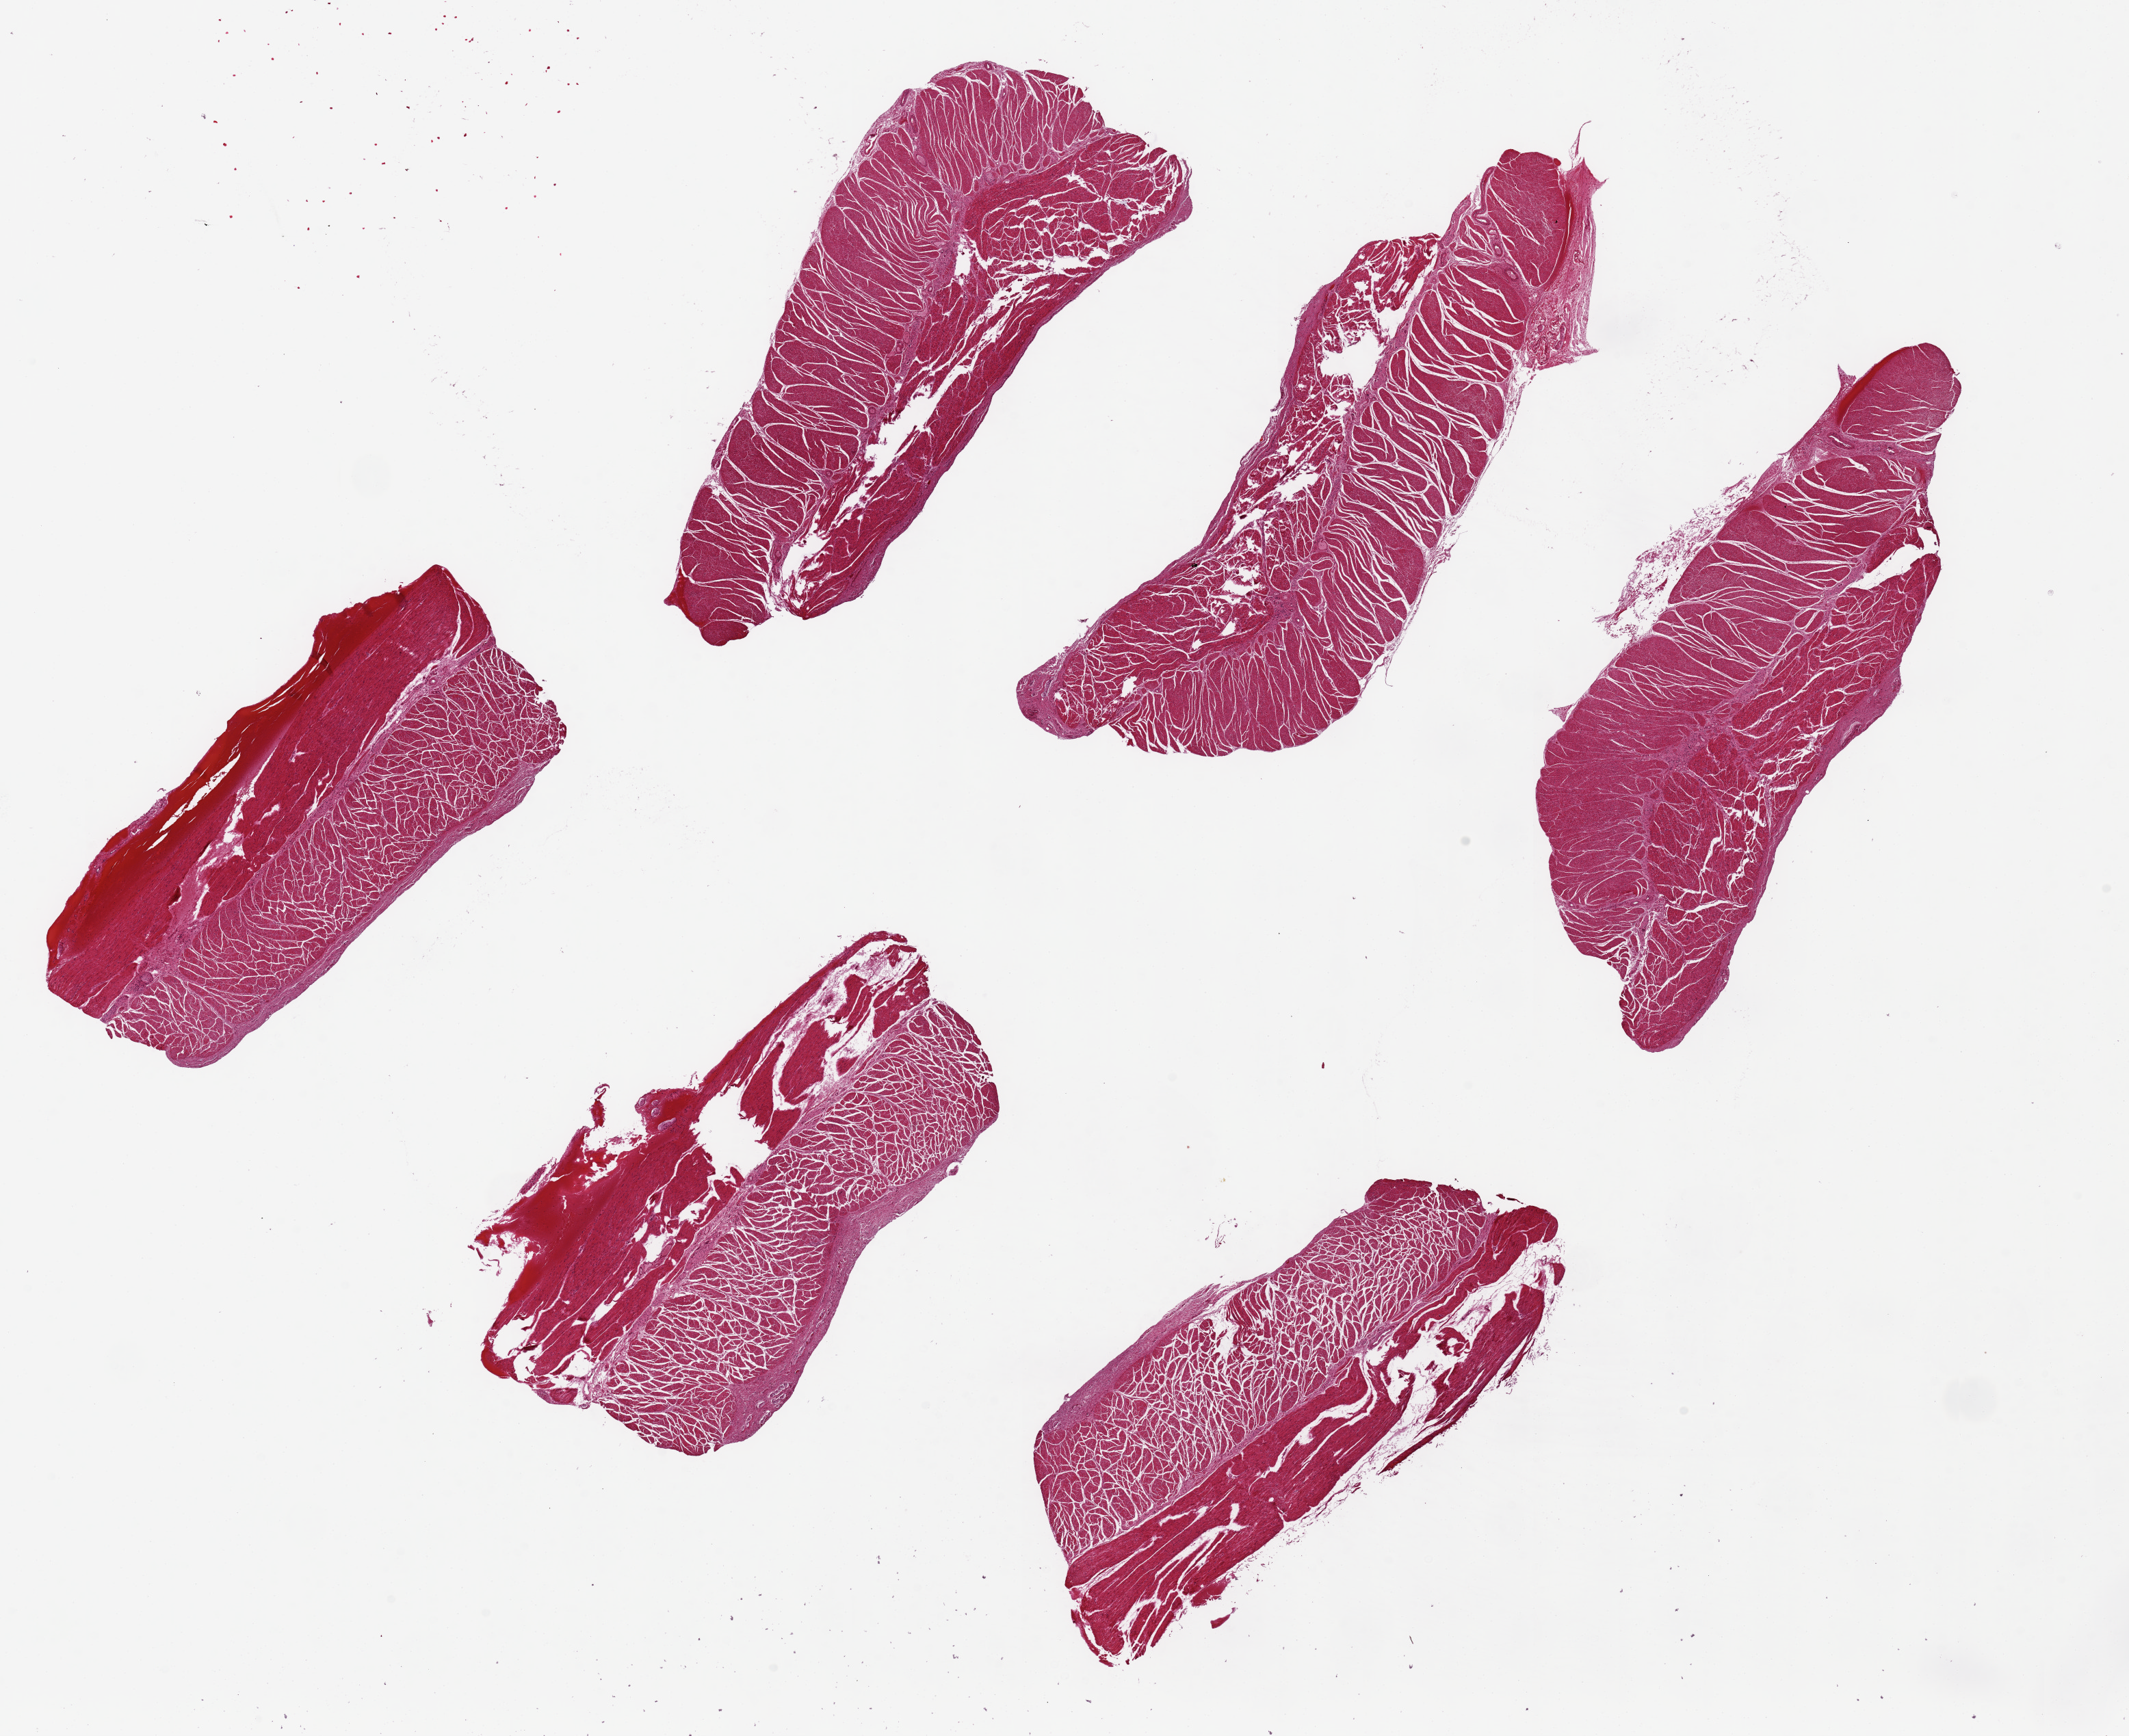
Digitized H&E-stained section — low-resolution overview of the scanned area, about 24.6 x 20.1 mm. PAXgene-fixed, paraffin-embedded tissue. Target tissue: esophageal muscle. Tissue donor sample. Female donor.
• review note (as recorded): 6 pieces up to 7x3 mm; clean adventitia